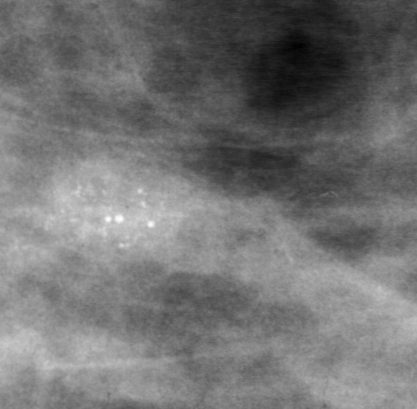
Crop from a digitized film mammogram around one marked abnormality, left breast, MLO view, BI-RADS breast density category 3 (scale 1–4).
Marked abnormality: calcifications, morphology round and regular / pleomorphic, distribution clustered; BI-RADS assessment category 0; pathology result (as recorded, not read from the image): benign.